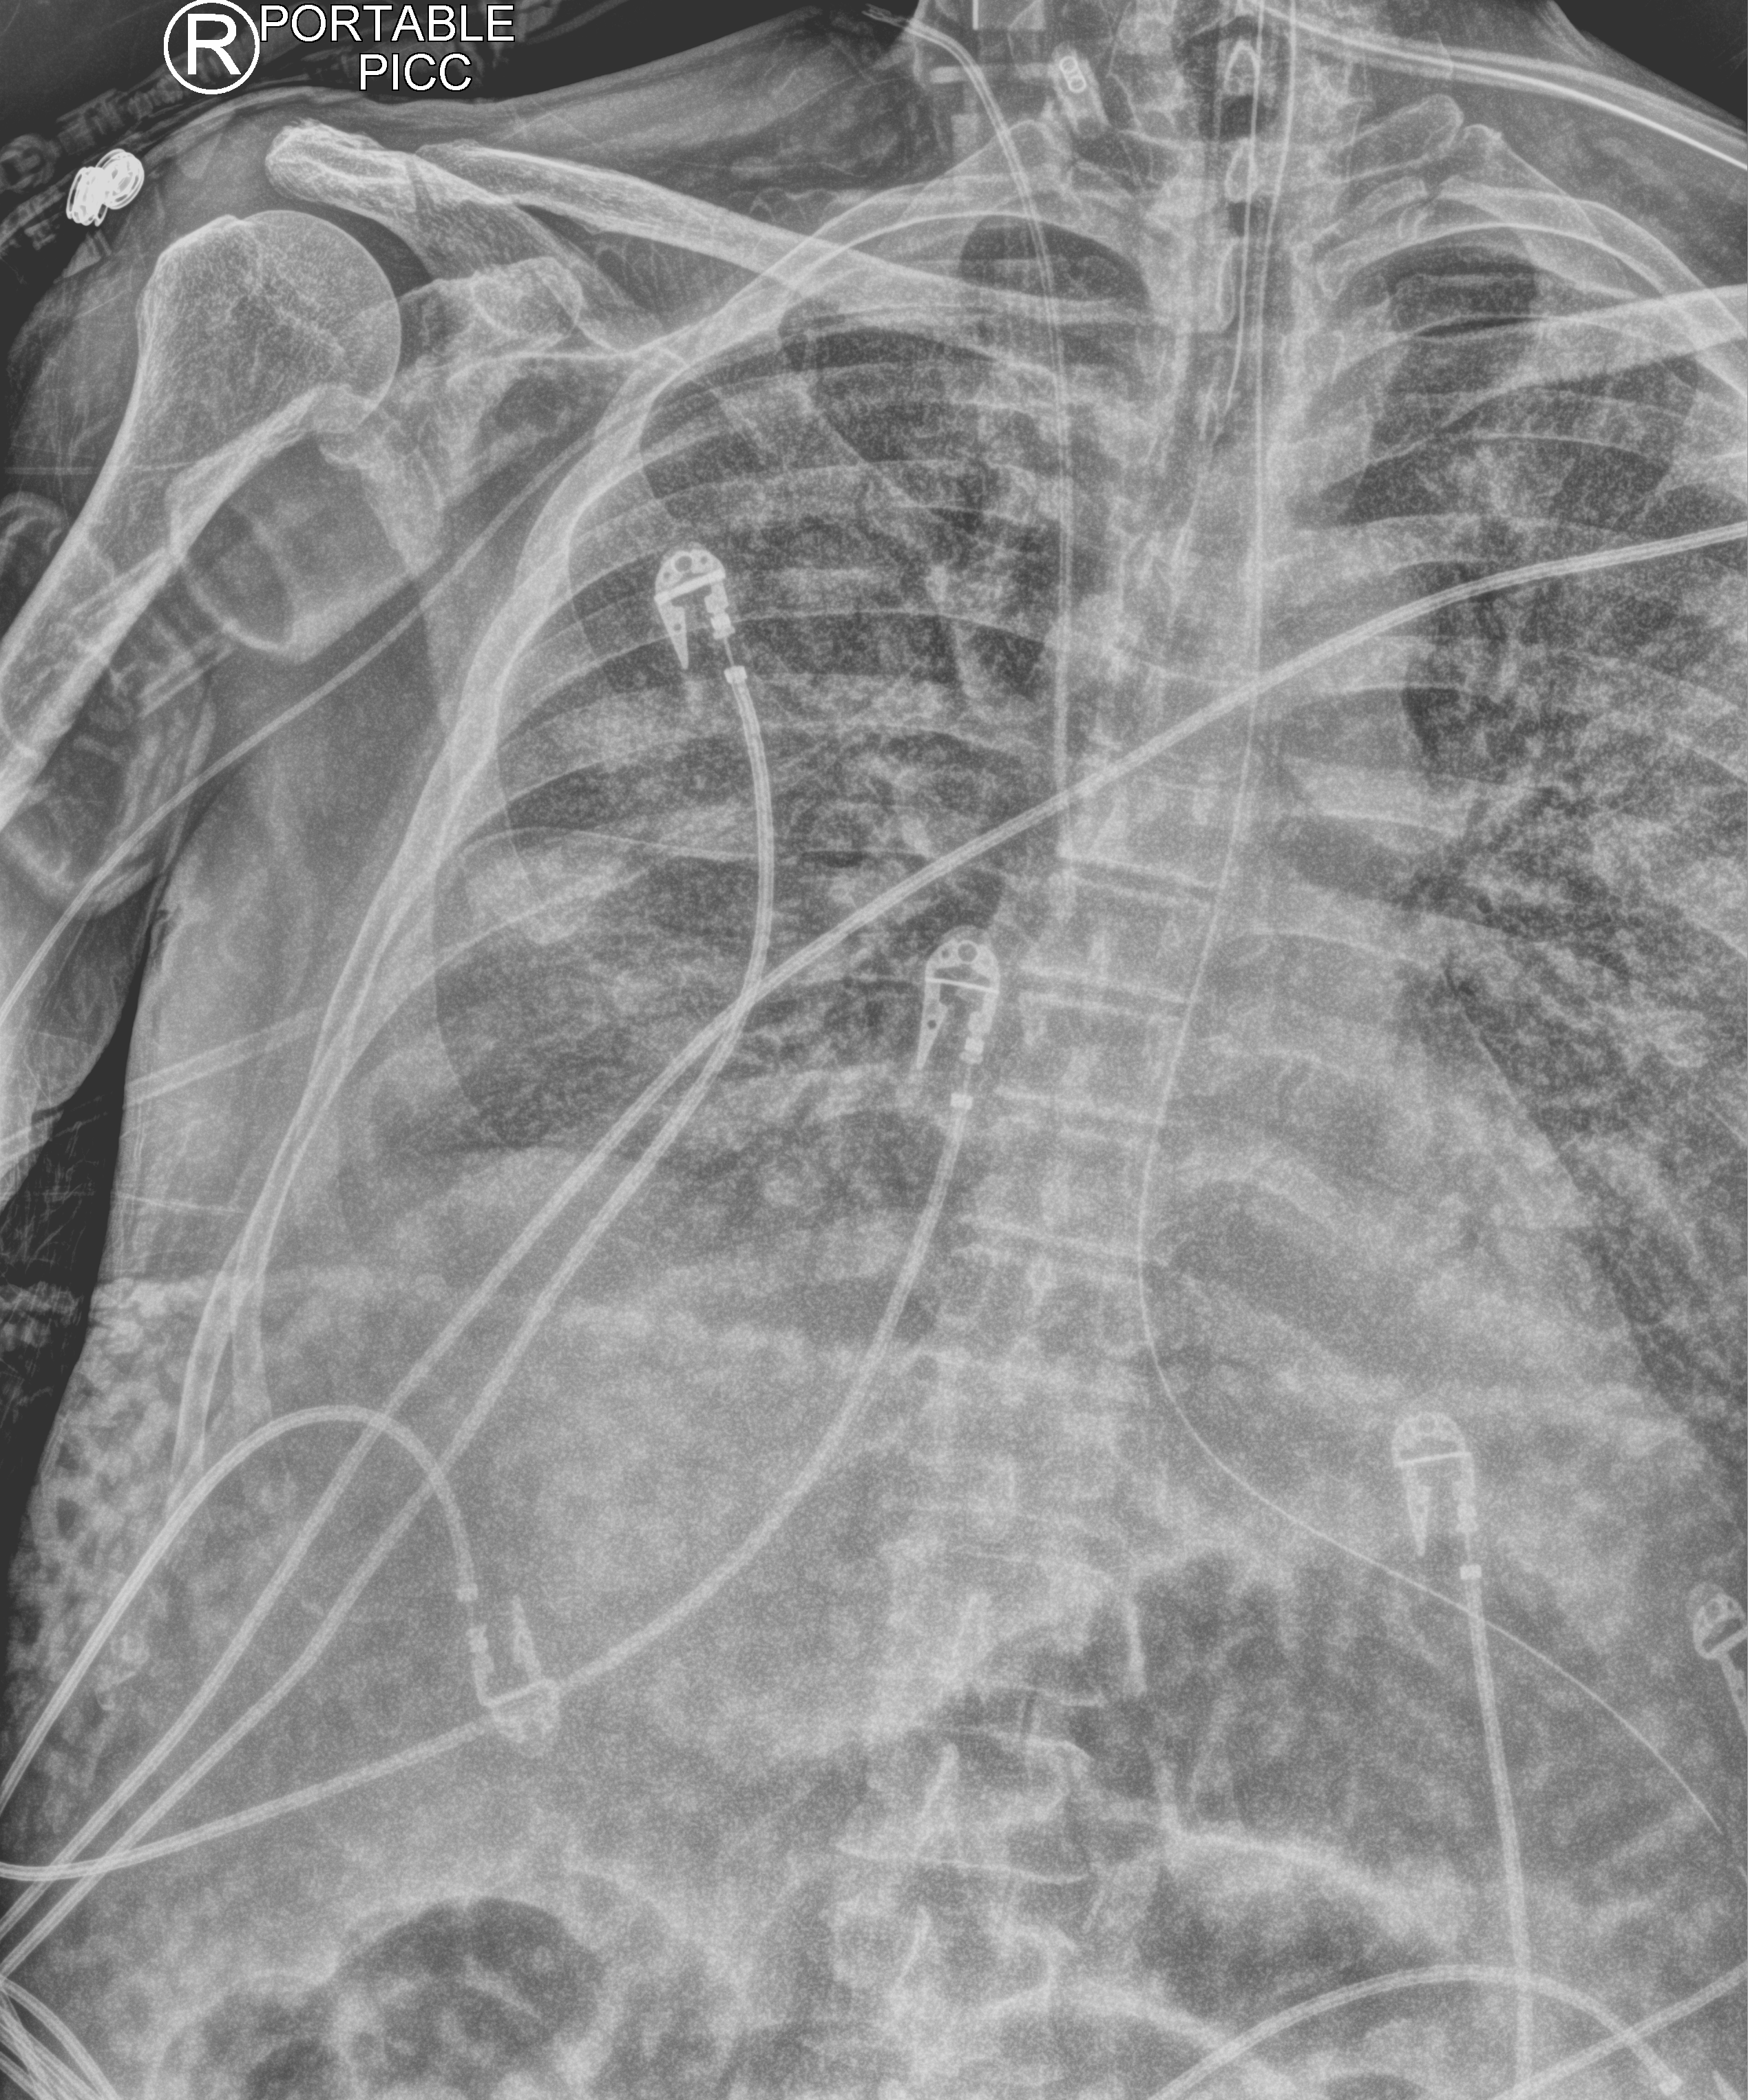
Portable chest radiograph, anteroposterior (AP) projection. Patient hospitalised with COVID-19; male, aged 60–74 years.
Hospital-stay facts (about this admission, not read from this image; timing relative to this image not recorded):
- diabetes (admission record): yes
- admitted to intensive care during this hospital stay: yes